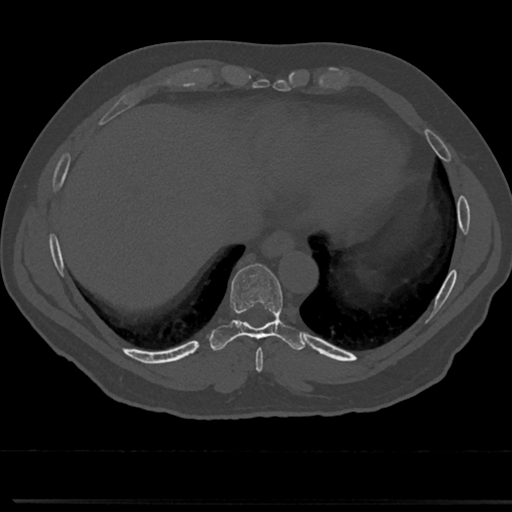
CT including the spine, one axial slice. Position 308 of 817 along the scan axis. 120 kVp. Bone window (W 1800 / L 400 HU). 512 × 512 image matrix, field of view 355 × 355 mm. Patient: male, 61 years. From the clinical record (not read from this slice): primary cancer: prostate.
Structures marked on this image (semi-automatically segmented with operator editing):
- T8 vertebra: bounding box <232,295,287,354> (left, top, right, bottom; pixels)
- T9 vertebra: <232,267,283,329>